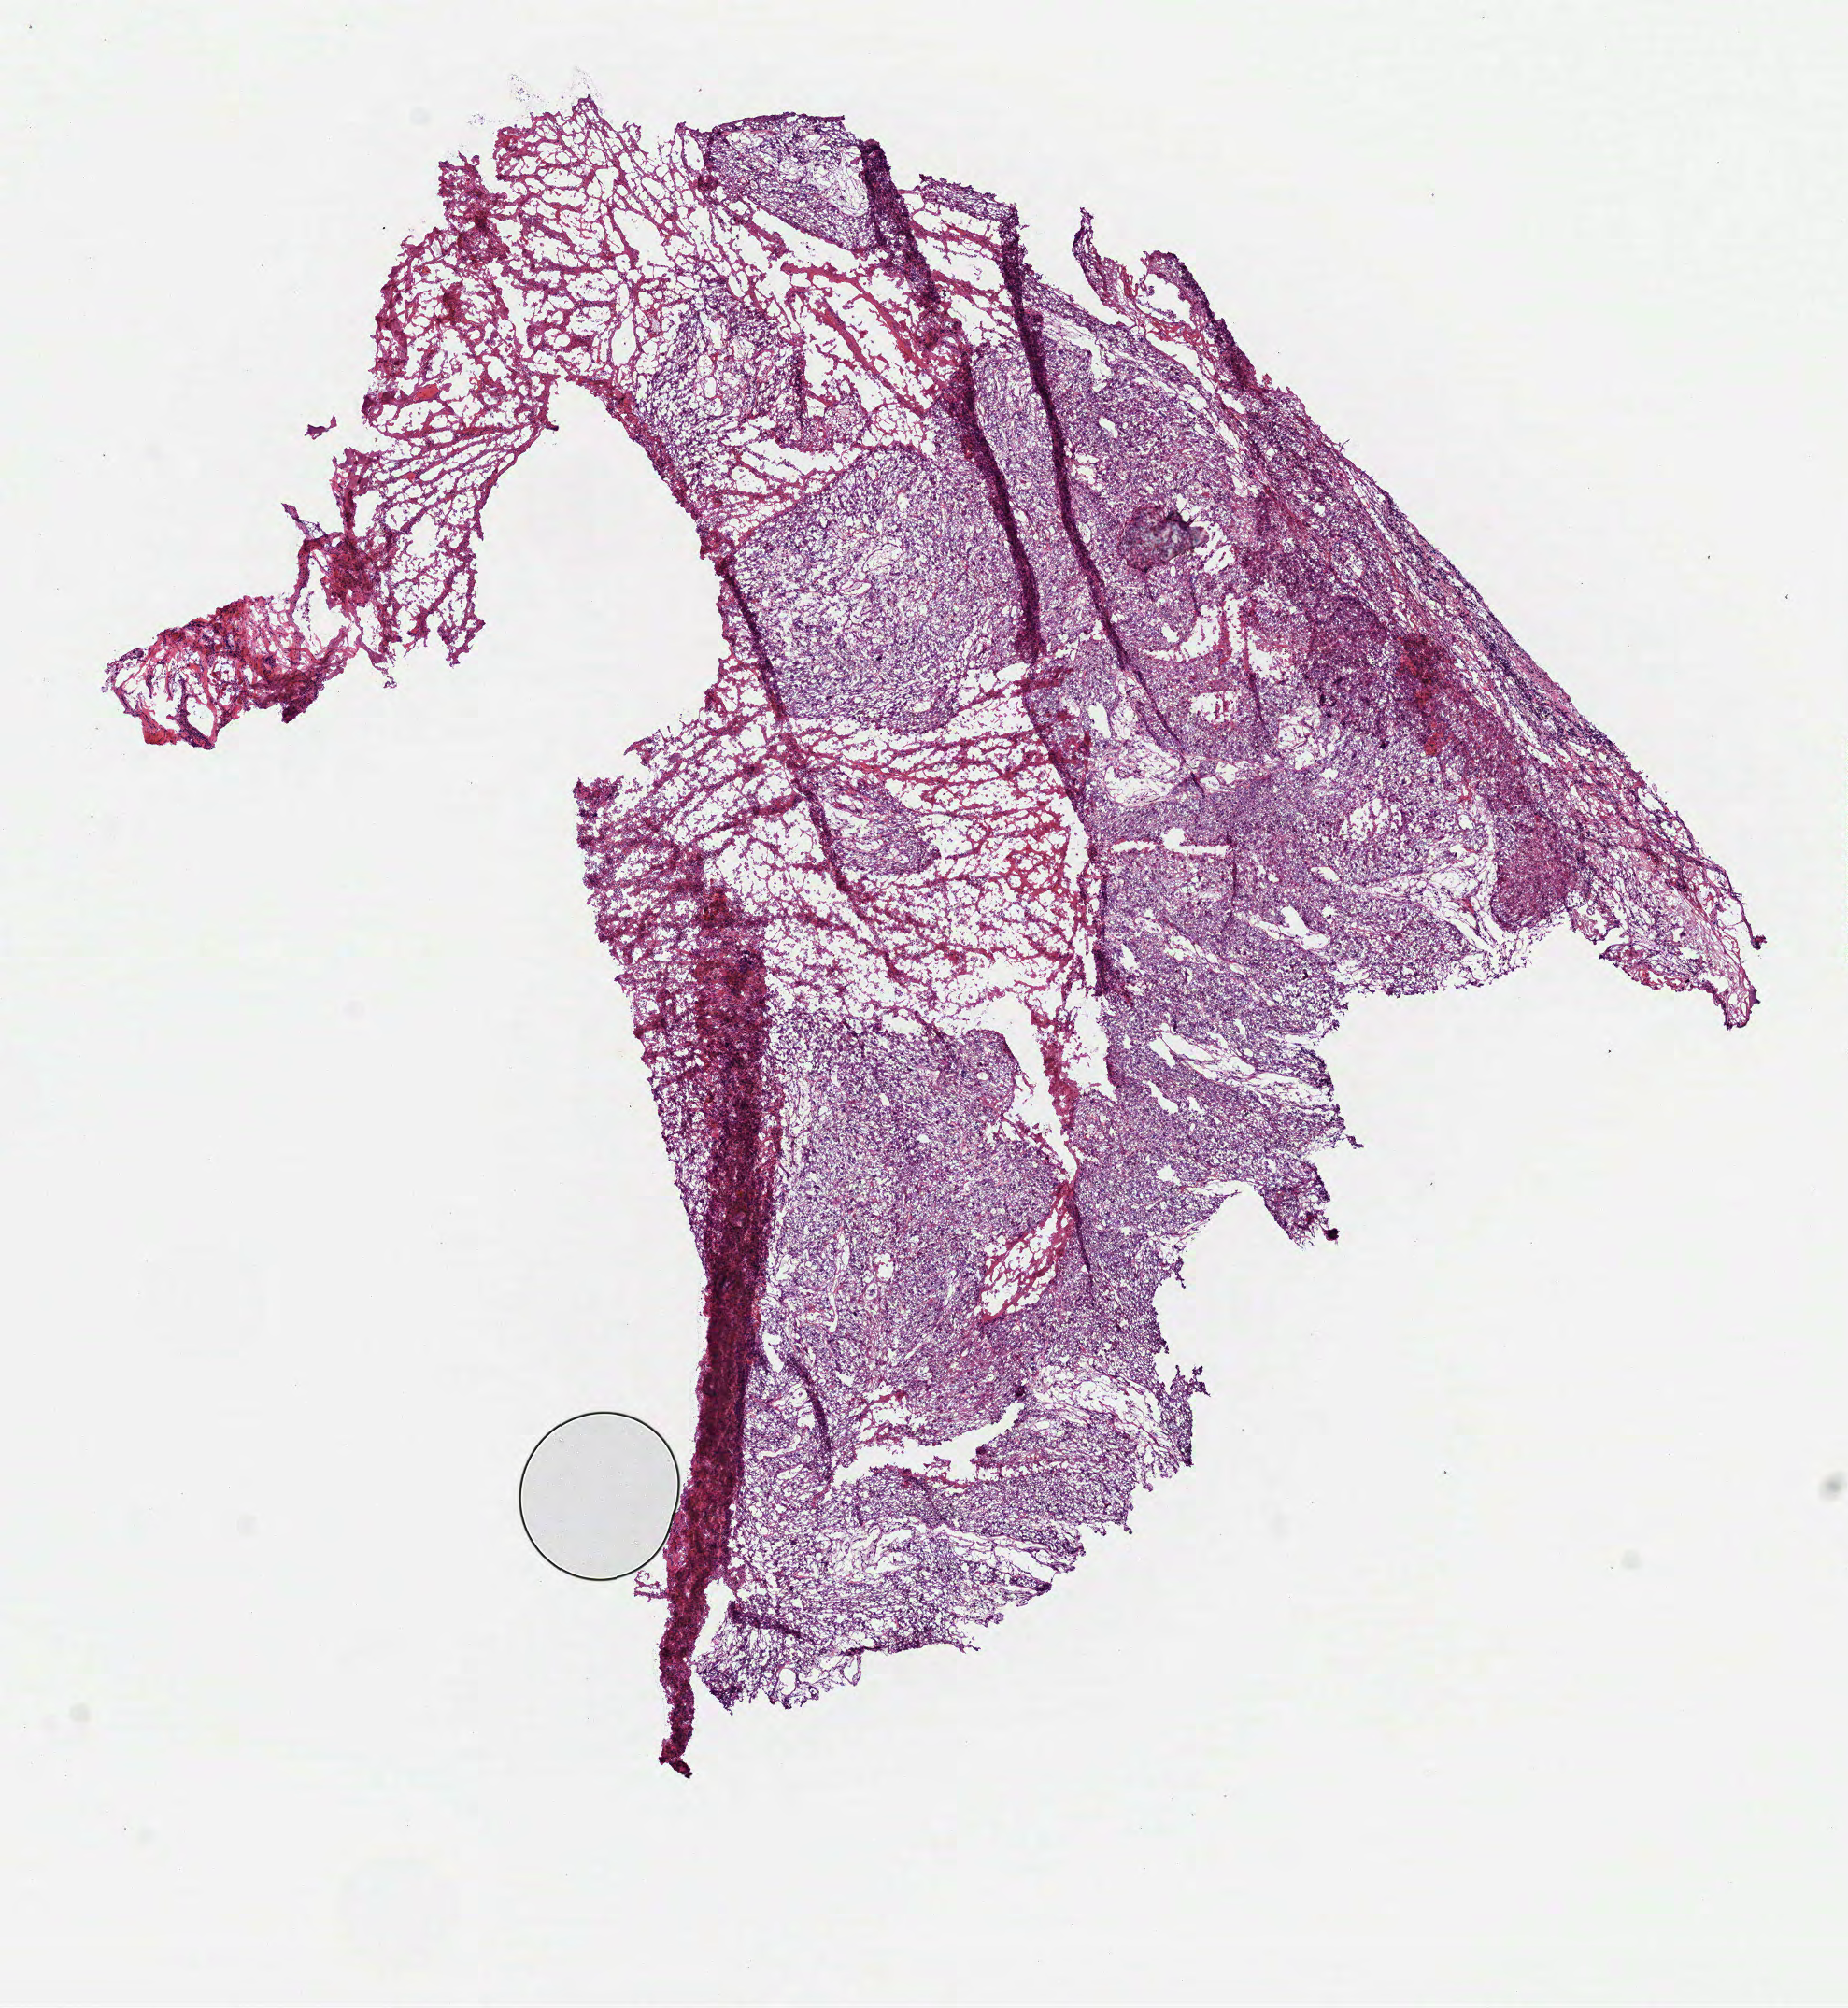
Whole-slide histology image, H&E, a low-resolution overview of the entire scanned area, about 8.0 x 8.7 mm (acquisition: 40x scan); frozen section; sample: primary tumour, head and neck. Male patient; age at initial diagnosis 48 years. Histologic grade: G2 (moderately differentiated). Slide review estimates, as recorded: tumour cells 75%, tumour nuclei 80%, normal cells 0%, stromal cells 0%, necrosis 25%. Infiltration values recorded for this section: lymphocyte infiltration 5%, monocyte infiltration 0%, neutrophil infiltration 5%.
Pathologic diagnosis: Squamous cell carcinoma, NOS (tongue, NOS). AJCC pathologic stage: III (7th edition).